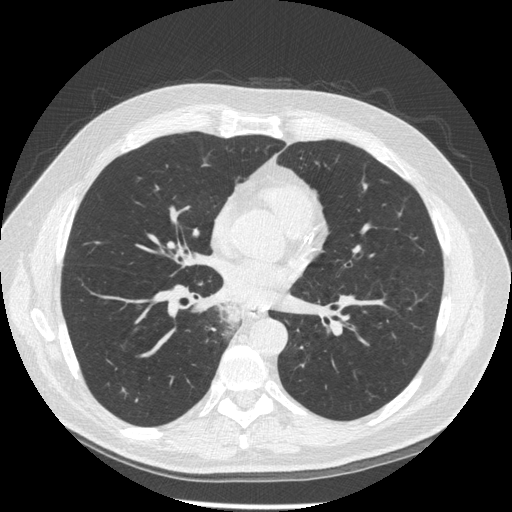
Low-dose screening chest CT, one axial slice. Slice 91 of 181 in the series (ordered by position). Lung window (W 1500 / L -600 HU). 1.25 mm slice thickness. 512 × 512 image matrix, field of view 370 × 370 mm.
Structures marked on this image (expert manual segmentation):
- lesion 1 (tumor, lower lobe of right lung): box from (x=218, y=303) to (x=240, y=327) px